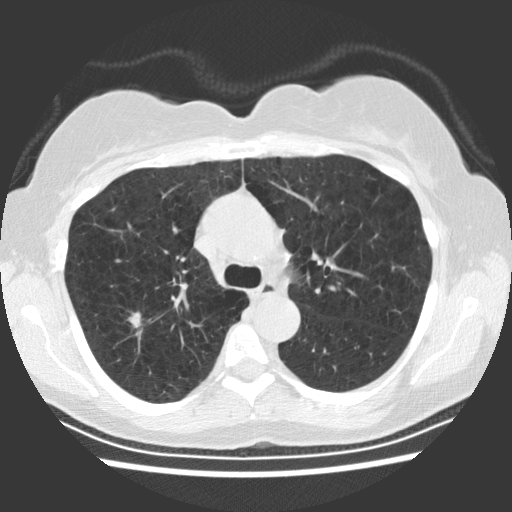
Low-dose screening chest CT, axial slice. Baseline screening round. Lung window (W 1500 / L -600 HU). 2.5 mm slice thickness. Standard (soft-tissue) reconstruction kernel (STANDARD). Slice 74 of 234 in the series. 512 × 512 image matrix, field of view 330 × 330 mm. Female participant, aged 66 years at enrolment. Former smoker at enrolment.
• Expert reader's lesion annotation, box from (x=110, y=303) to (x=153, y=341) px.
• Screening reader's record for this exam (one nodule recorded; not confirmed to be the boxed lesion): non-calcified nodule or mass ≥4 mm, right upper lobe, 10 × 8 mm, smooth margins, soft tissue attenuation.
• Official screen result: positive, change unspecified: nodule(s) >= 4 mm or enlarging nodule(s), mass(es), or other non-specific abnormalities suspicious for lung cancer.
• Lung cancer was diagnosed 54 days after this screen: squamous cell carcinoma, keratinizing, NOS, right upper lobe, poorly differentiated (G3), stage IA (AJCC 6th edition), 11 mm at pathology.